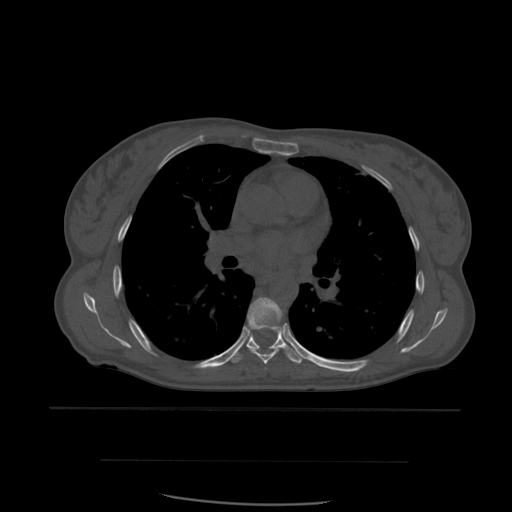
CT including the spine, one axial slice; position 384 of 574 along the scan axis; bone window (W 1800 / L 400 HU); 1.25 mm slice thickness; 512 × 512 image matrix, field of view 392 × 392 mm. Patient age 48 years. From the clinical record (not read from this slice): primary cancer: lung; vertebrae with lytic lesions (as recorded): T11.
Structures marked on this image (semi-automatic segmentation, software-assisted and operator-edited):
- T6 vertebra: bounding box <246,297,285,365> (left, top, right, bottom; pixels)
- T7 vertebra: <229,328,304,364>